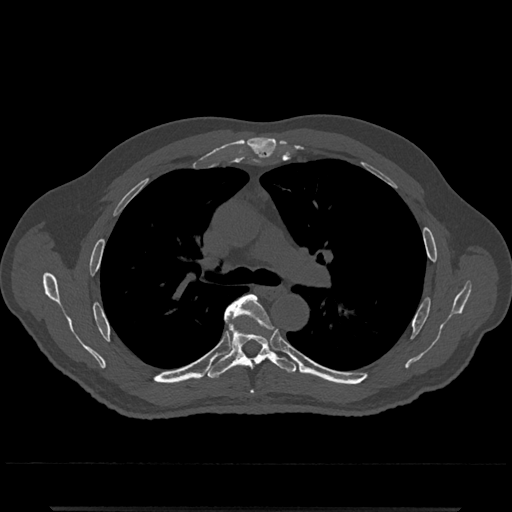
CT including the spine, one axial slice. Position 792 of 797 along the scan axis. Reconstruction kernel Br40s/3. 120 kVp. Bone window (W 1800 / L 400 HU). 0.5 mm slice thickness. 512 × 512 image matrix, field of view 393 × 393 mm. Male patient, age 67 years. Case-level facts recorded for this patient, not image findings: primary cancer: prostate.
Structures marked on this image (semi-automatic segmentation, software-assisted and operator-edited):
- T5 vertebra: box from (x=226, y=294) to (x=269, y=325) px
- T6 vertebra: (x=205, y=302)–(x=297, y=379)